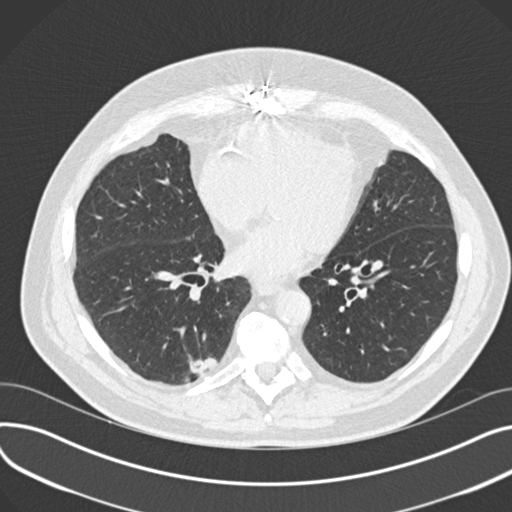
Axial slice from a low-dose chest CT screening exam; third screening round (two years after baseline); lung window (W 1500 / L -600 HU); 2 mm slice thickness; slice 103 of 177 in the series; 512 × 512 image matrix. Male, age 68 years at enrolment. Former smoker at enrolment.
Lesion marked by an expert reader, box from (x=176, y=346) to (x=220, y=385) px. The screening reader recorded 4 non-calcified nodules or masses ≥4 mm on this exam; which of them this box marks is not recorded.